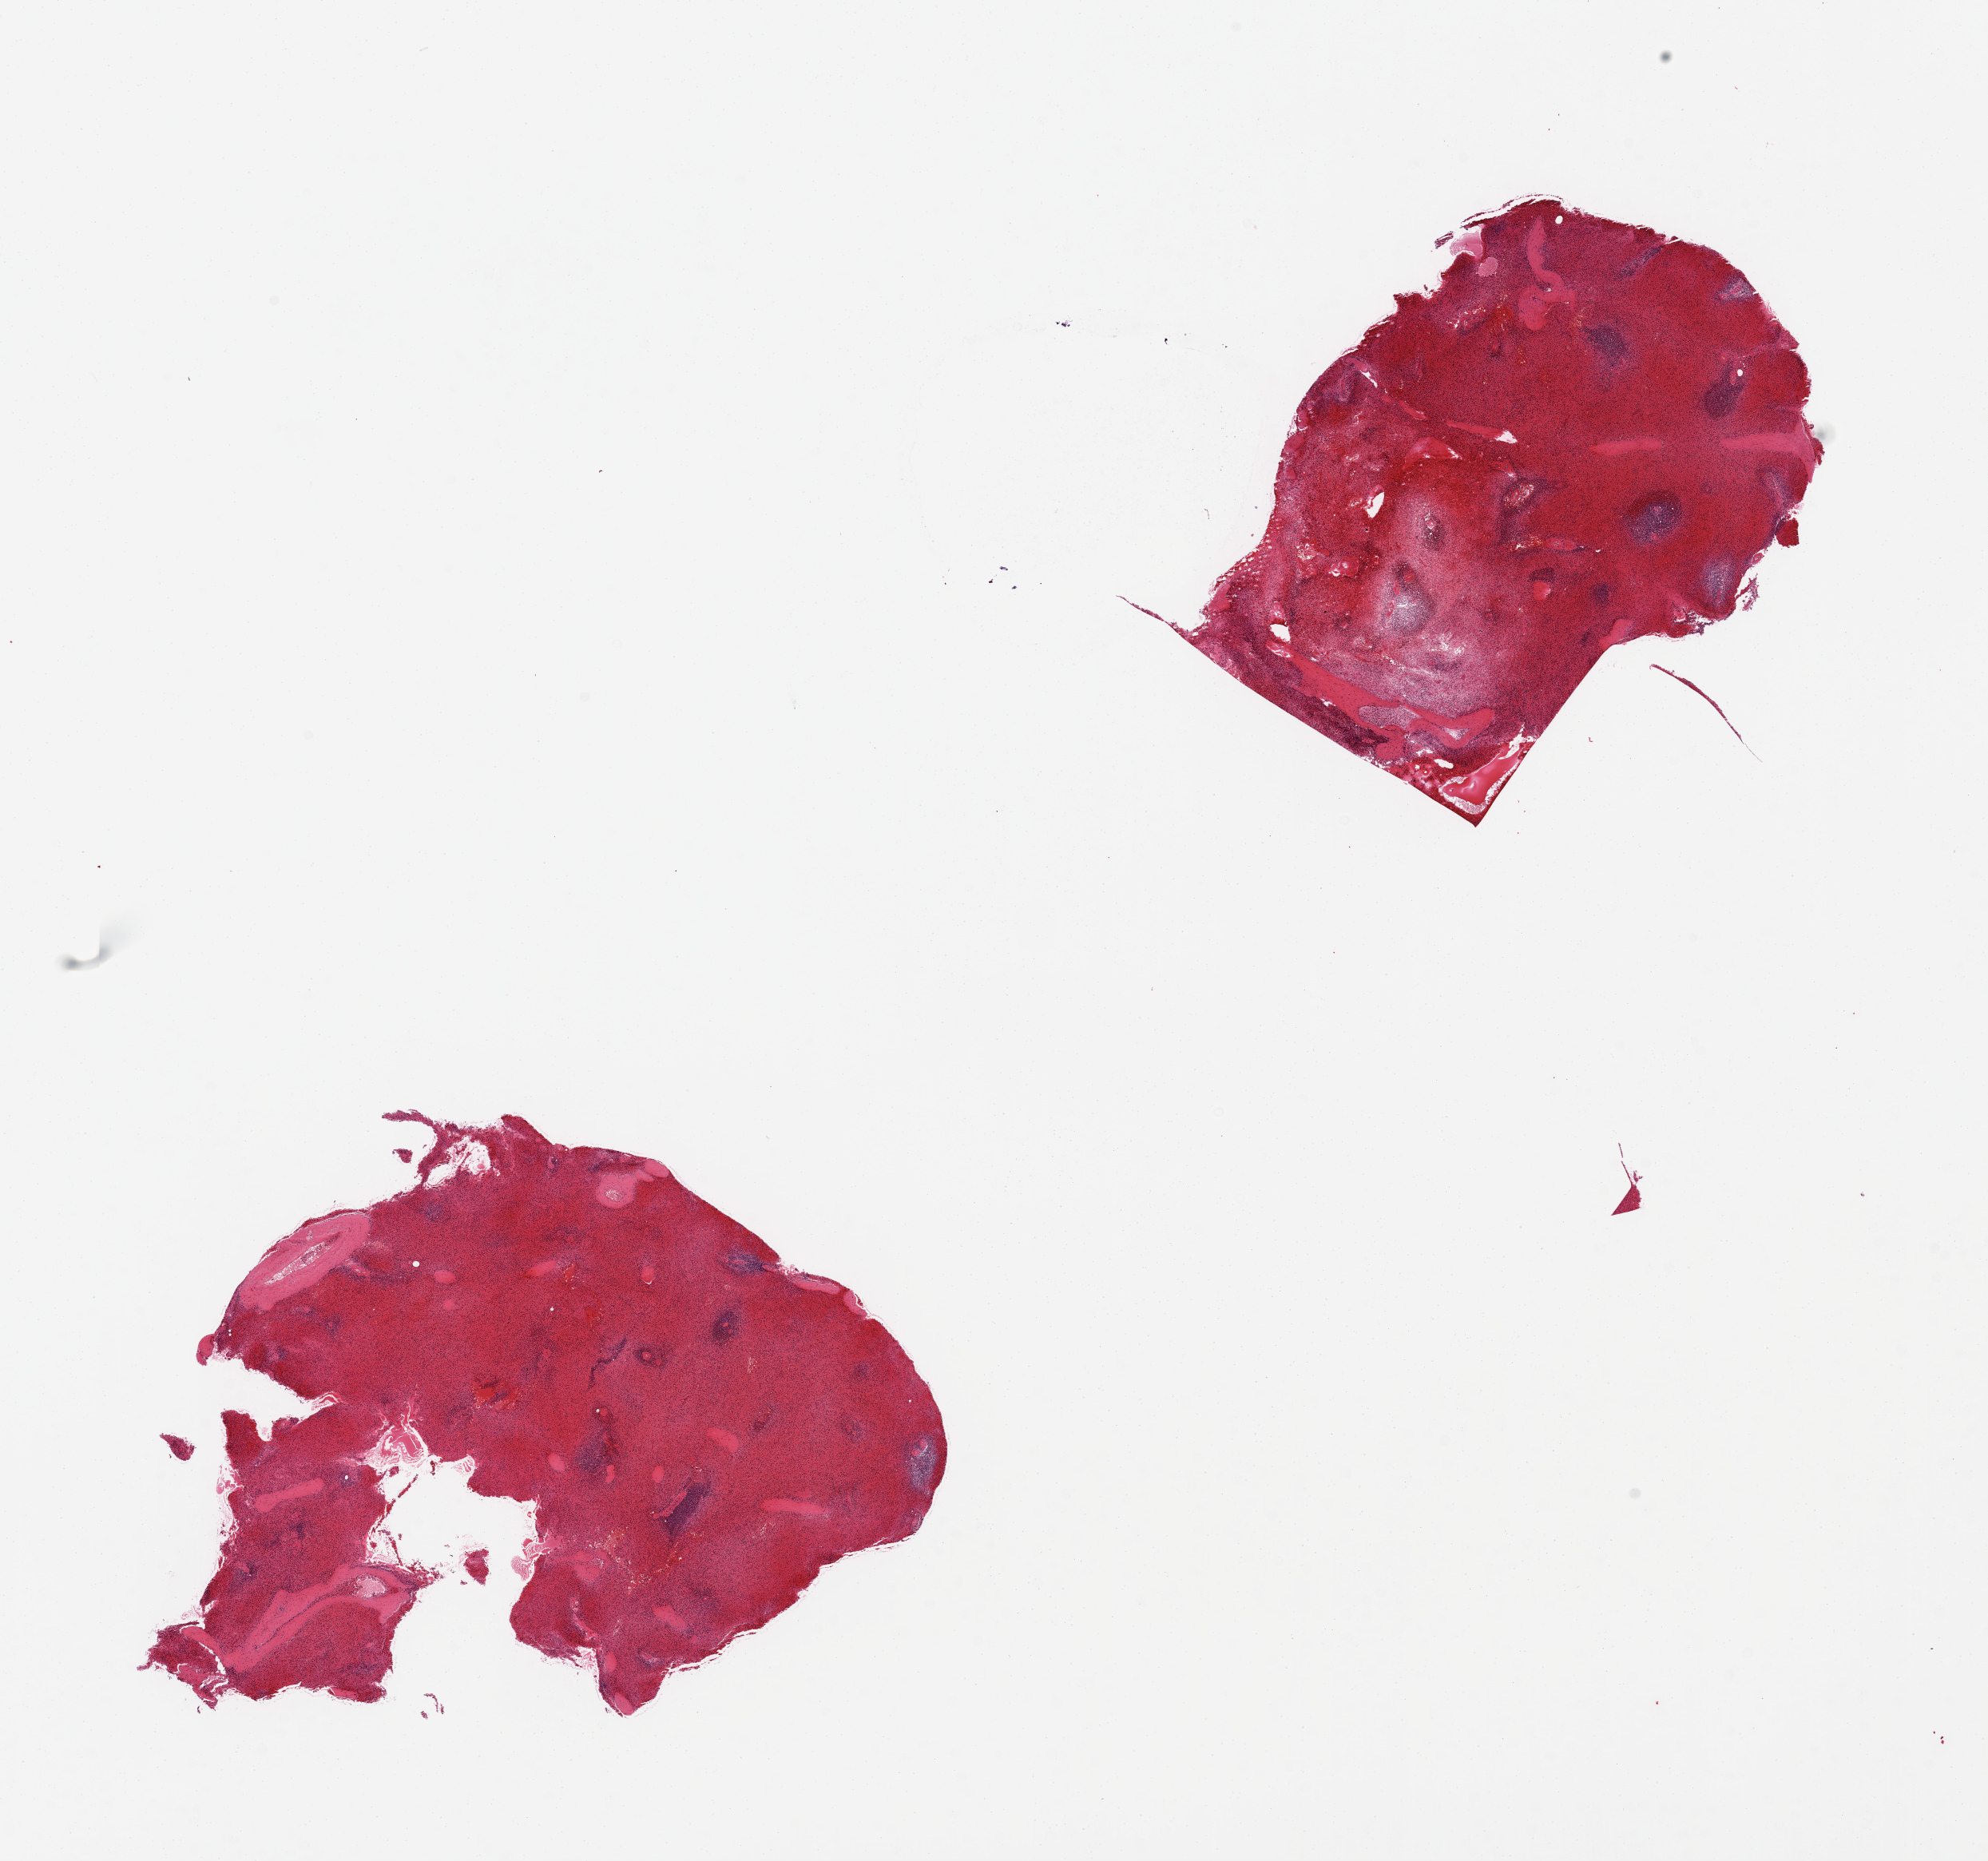
Digitized hematoxylin and eosin (H&E)-stained section, brightfield, shown as a low-resolution overview of the whole scanned area (about 19.7 x 18.4 mm, acquisition: 20x scan); PAXgene-fixed paraffin-embedded (PFPE) section; section of spleen (target tissue); tissue donor sample. Donor: male.
• pathologist's review note for this sample: 2 pieces, congested